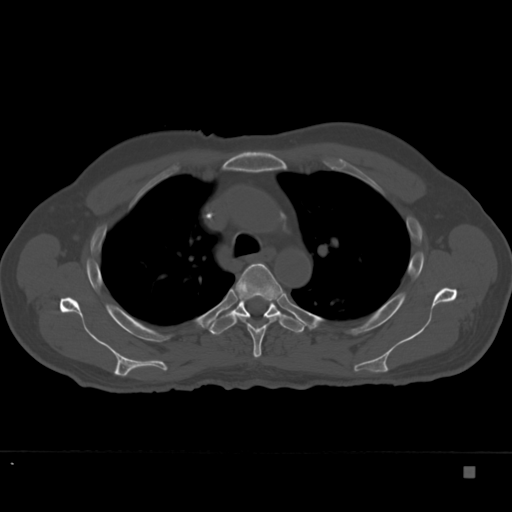
CT including the spine, one axial slice. Position 264 of 332 along the scan axis. Reconstruction kernel Br40s. 120 kVp. Bone window (W 1800 / L 400 HU). 512 × 512 image matrix, field of view 389 × 389 mm. Male patient, age 72 years. Case-level facts recorded for this patient, not image findings: primary cancer: skeletal.
Annotated regions visible in this slice (semi-automatically segmented with operator editing):
- T4 vertebra: box from (x=233, y=263) to (x=285, y=358) px
- T5 vertebra: (x=209, y=298)–(x=304, y=335)